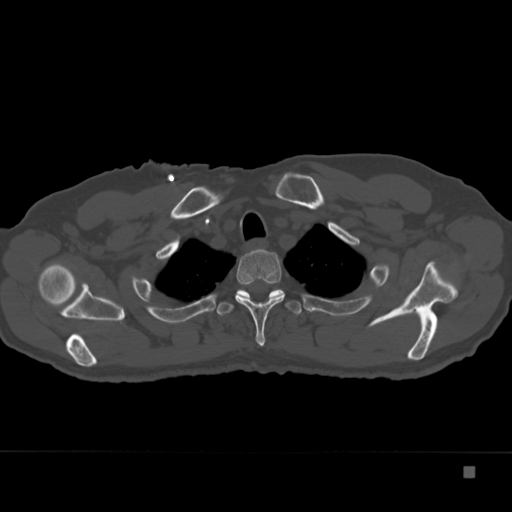
CT including the spine, one axial slice. Position 297 of 332 along the scan axis. Bone window (W 1800 / L 400 HU). 512 × 512 image matrix, field of view 389 × 389 mm. Male patient, age 72 years. From the clinical record (not read from this slice): primary cancer: skeletal.
Outlined on this slice (semi-automatic segmentation, software-assisted and operator-edited):
- T2 vertebra: bounding box <235,249,285,346> (left, top, right, bottom; pixels)
- T3 vertebra: <216,289,302,316>